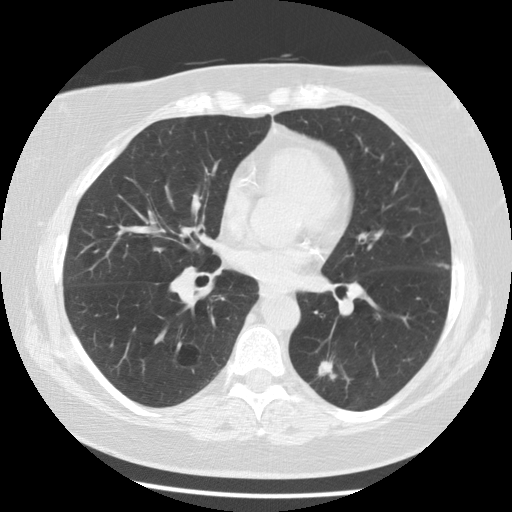
Low-dose screening chest CT, one axial slice. Slice 56 of 116 in the series (ordered by position). Lung window (W 1500 / L -600 HU). 2.5 mm slice thickness. 512 × 512 image matrix, field of view 341 × 341 mm.
Structures marked on this image (outlined manually by an expert reader):
- lesion 1 (tumor, lower lobe of left lung): bounding box [x1, y1, x2, y2] px = [318, 361, 333, 376]